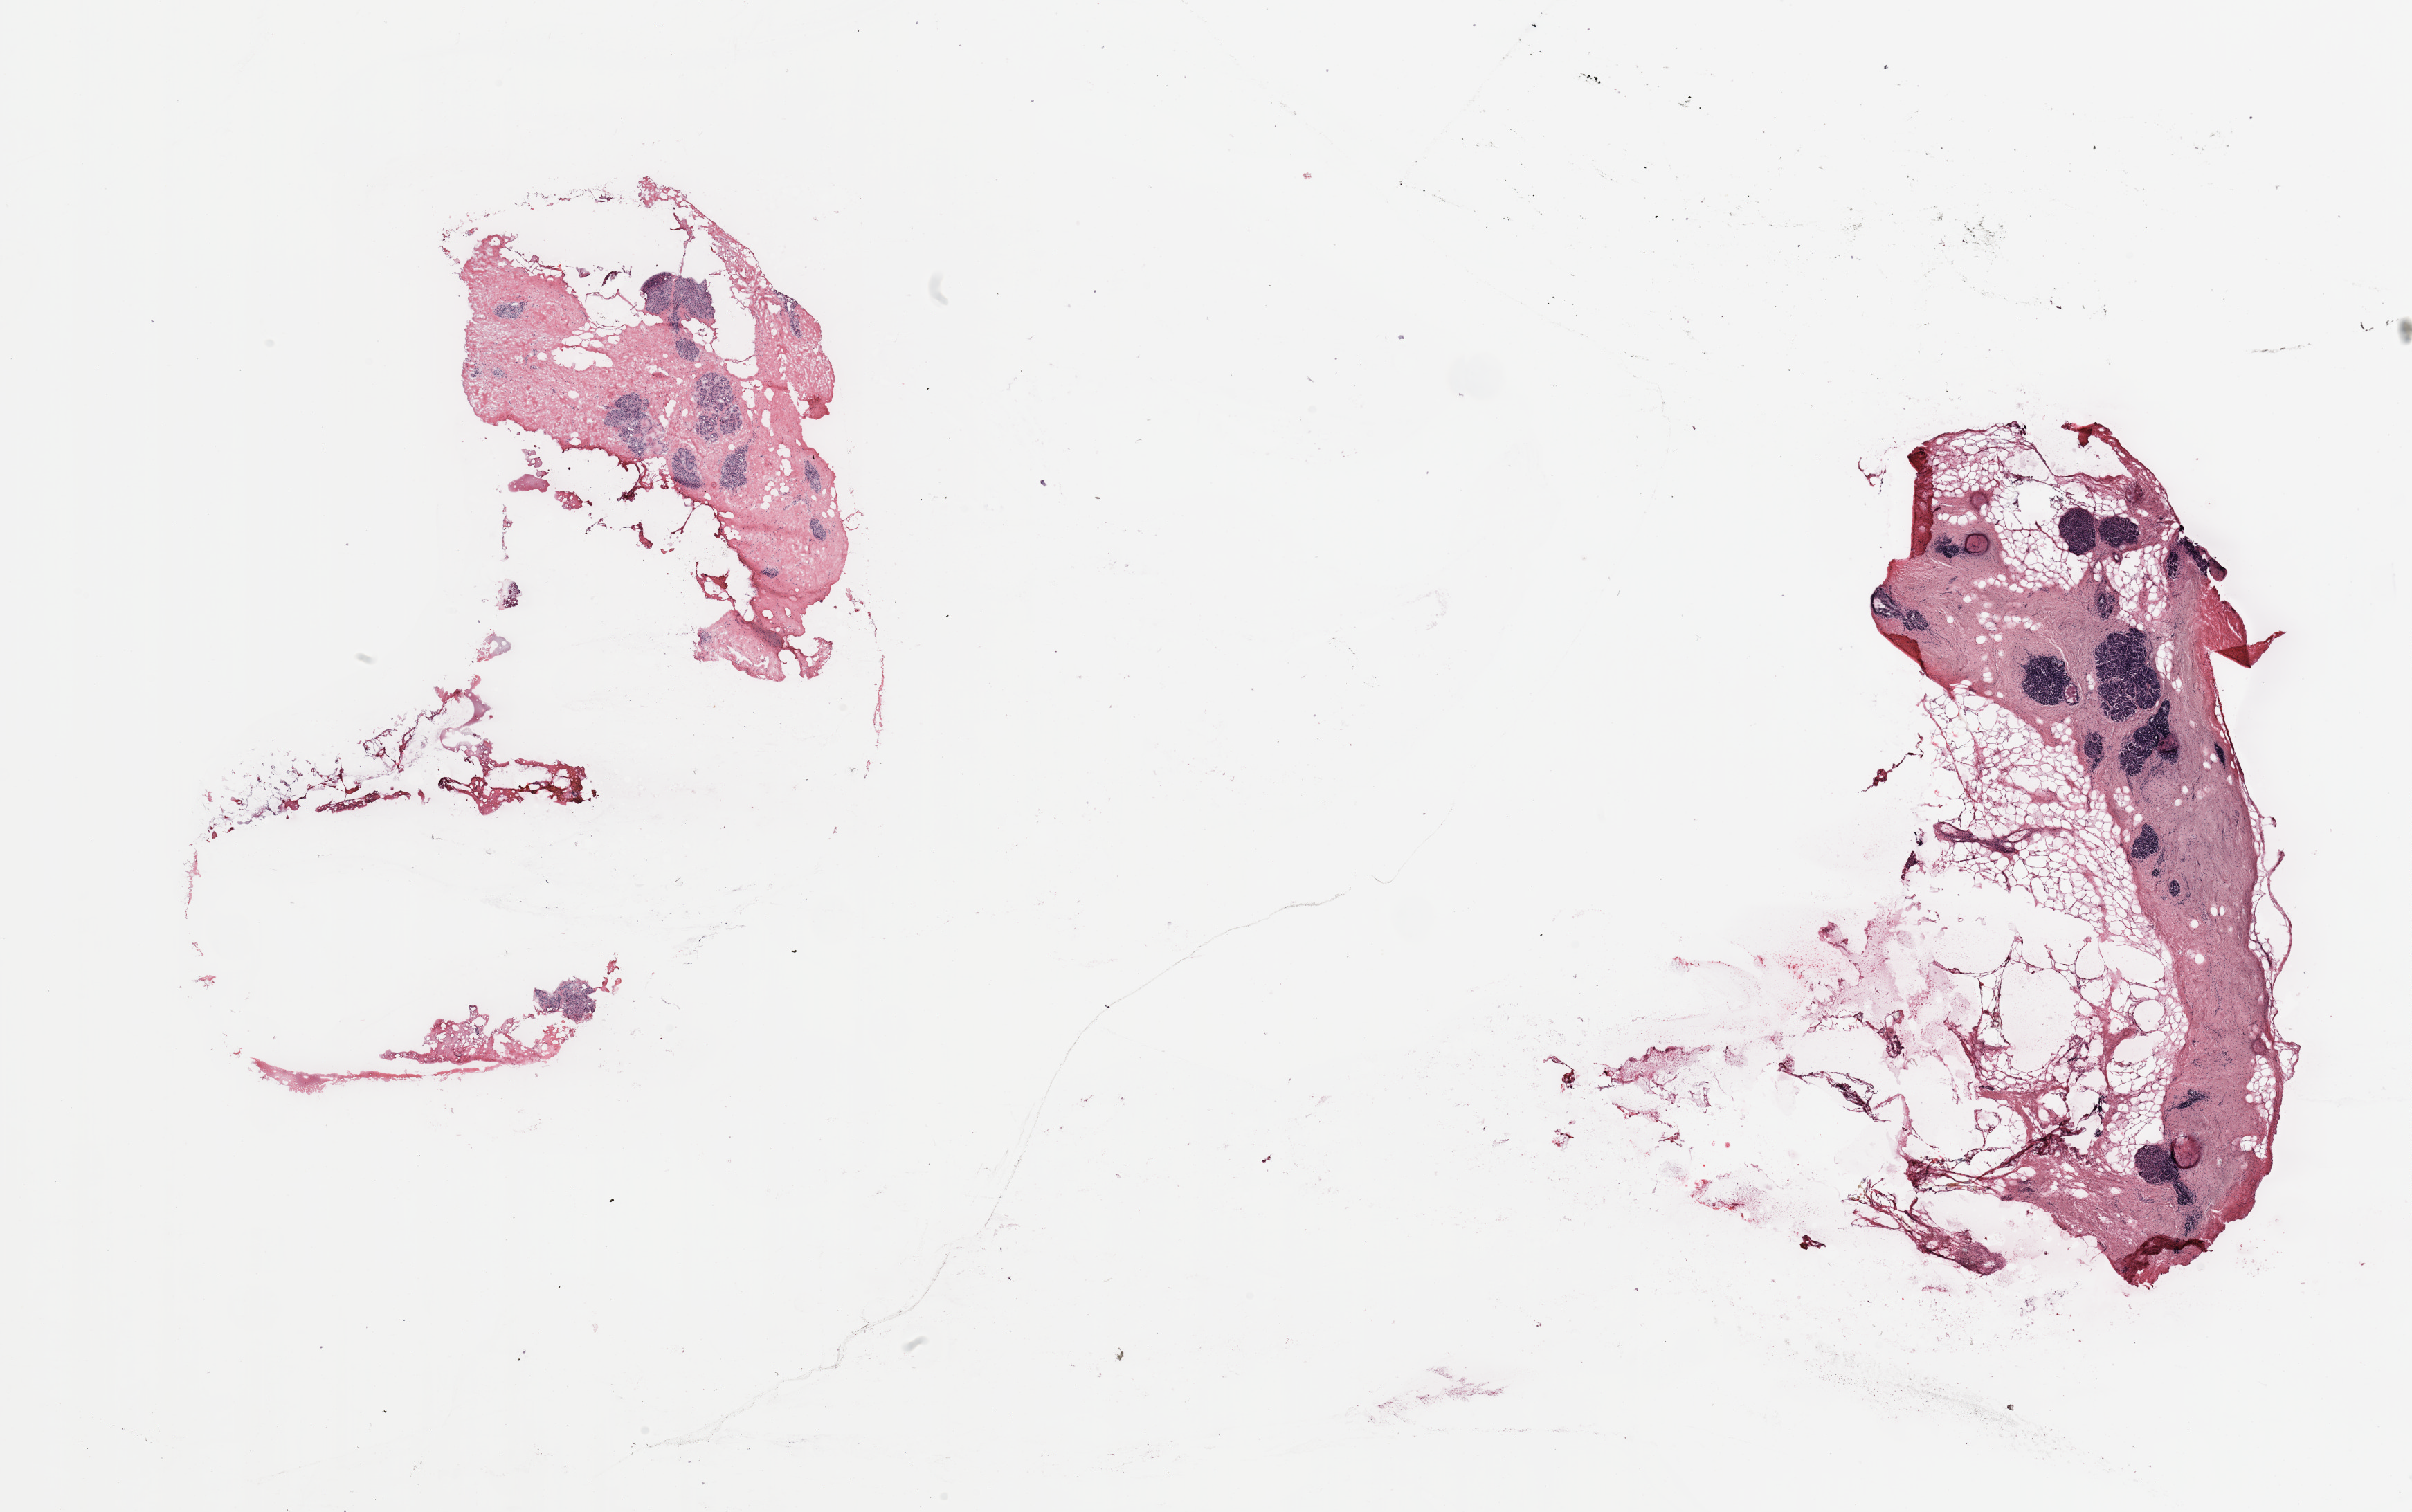
Whole-slide histology image, H&E-stained — a low-resolution overview of the entire scanned area, about 27.6 x 17.3 mm; breast, tissue type not recorded.
• patient diagnosis (cohort enrolment): breast cancer (breast)